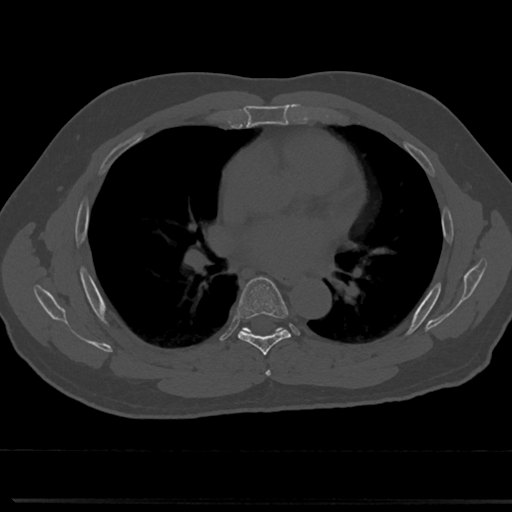
CT including the spine, one axial slice. Slice 446 of 817 in the series (ordered by position). Reconstruction kernel Br40s/3. 120 kVp. Bone window (W 1800 / L 400 HU). 0.5 mm slice thickness. 512 × 512 image matrix, field of view 355 × 355 mm. Patient: male, 61 years. Case-level facts recorded for this patient, not image findings: primary cancer: prostate.
Structures marked on this image (semi-automatically segmented with operator editing):
- T5 vertebra: bounding box <265,352,273,377> (left, top, right, bottom; pixels)
- T6 vertebra: <219,277,310,354>